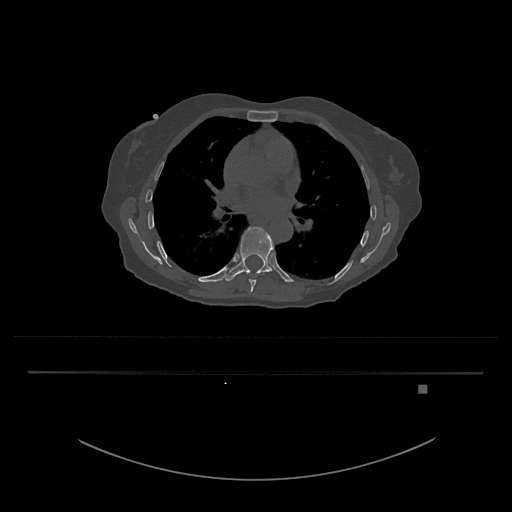
CT including the spine, one axial slice; position 776 of 797 along the scan axis; 120 kVp; bone window (W 1800 / L 400 HU); 0.5 mm slice thickness; 512 × 512 image matrix. Patient: female, 57 years. From the clinical record (not read from this slice): primary cancer: cervical.
Structures marked on this image (semi-automatically segmented with operator editing):
- T8 vertebra: box from (x=246, y=271) to (x=260, y=292) px
- T9 vertebra: (x=225, y=227)–(x=278, y=282)